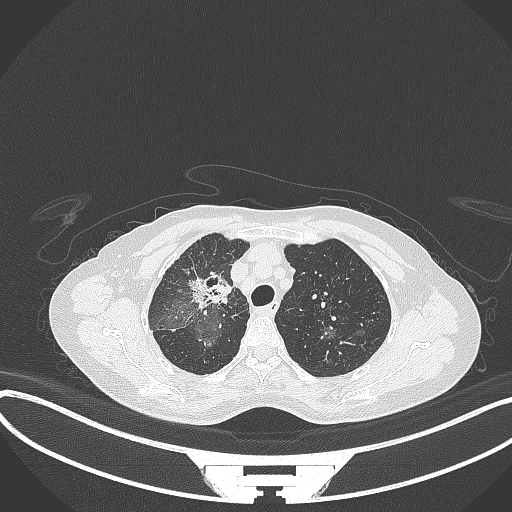
Chest CT, one axial slice; slice 247 of 284 in the series (ordered by position); 120 kVp; lung window (W 1500 / L -600 HU); 1 mm slice thickness; 512 × 512 image matrix, field of view 400 × 400 mm. Patient: female, 59 years. Case-level facts recorded for this patient, not image findings: clinical TNM (as recorded): T3 N0 M0.
Structures marked on this image (bounding box drawn by a radiologist):
- lung tumour (recorded histology: adenocarcinoma): bounding box (x1, y1, x2, y2) in pixels: (187, 268, 232, 310)